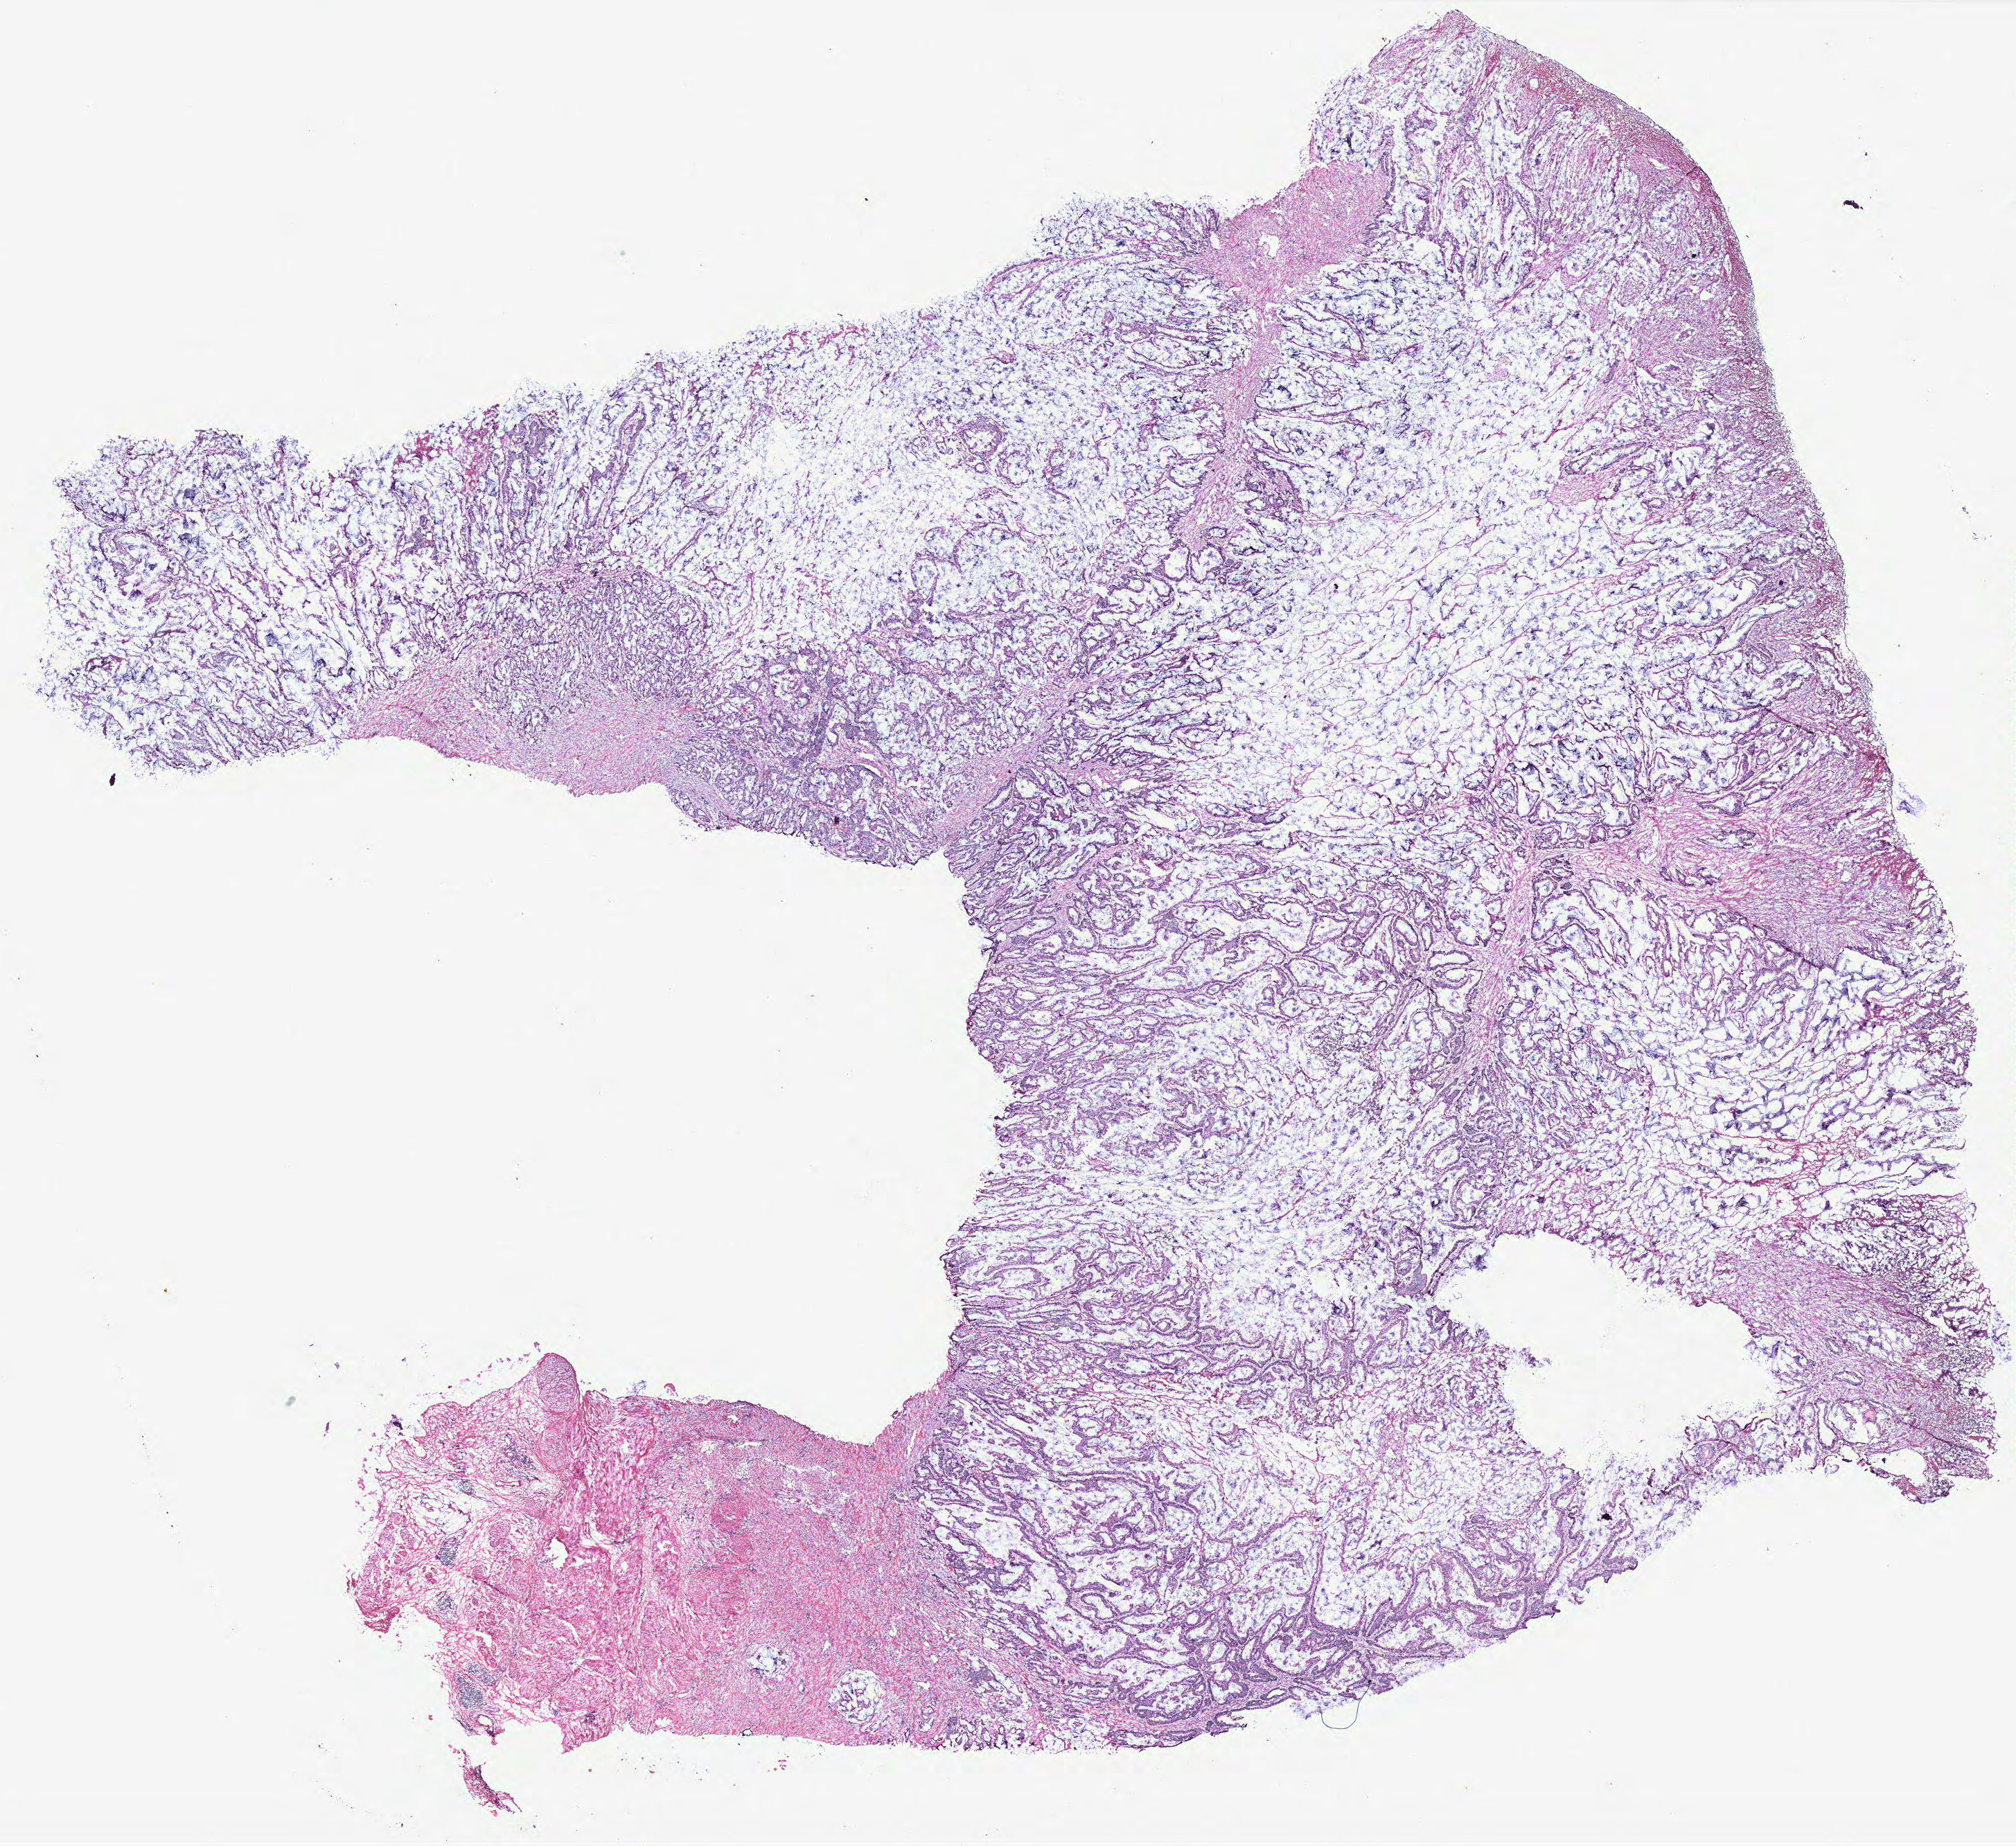
Whole-slide histology image, H&E-stained — shown as a low-resolution overview of the whole scanned area (about 23.3 x 21.3 mm); colon, tissue type not recorded.
• patient diagnosis (cohort enrolment): colon cancer (colon)